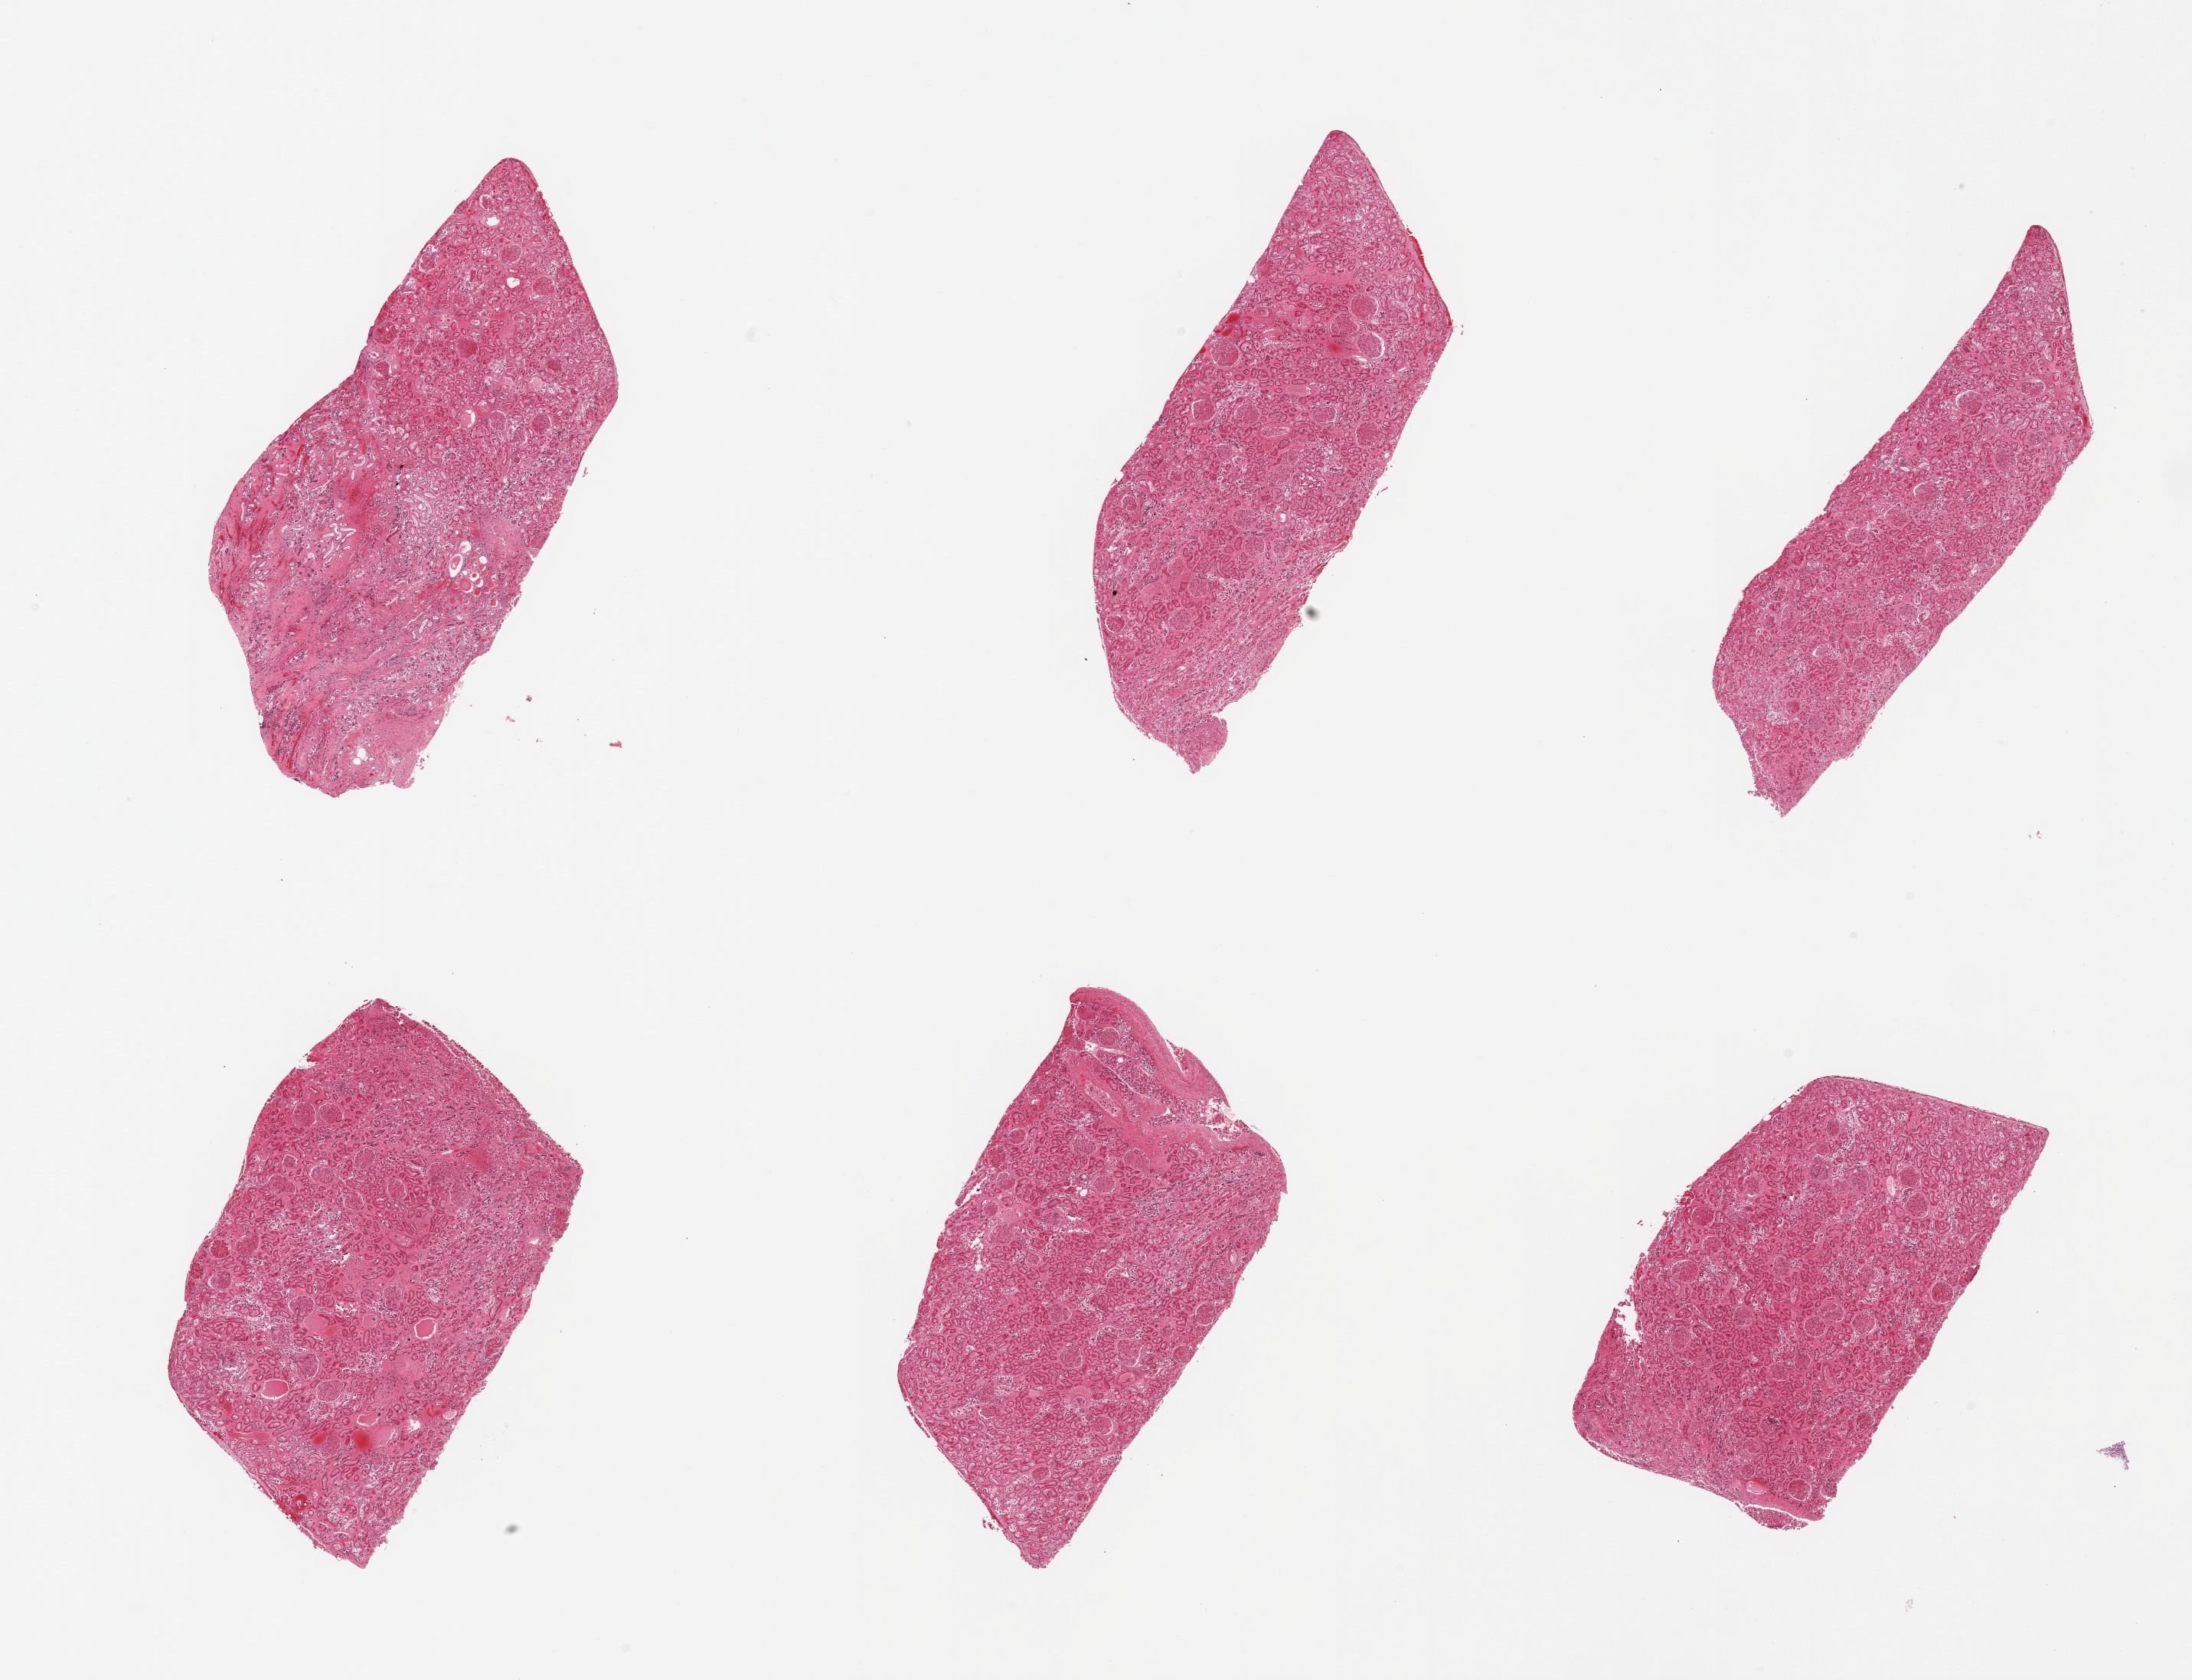
Whole-slide image, haematoxylin and eosin stain, a low-resolution overview of the entire scanned area, about 22.6 x 17.4 mm; PAXgene-fixed, paraffin-embedded tissue; sampled site (target tissue): renal cortex; tissue donor sample.
• review note (as recorded): 6 pieces; glomeruli in all sections; congestion